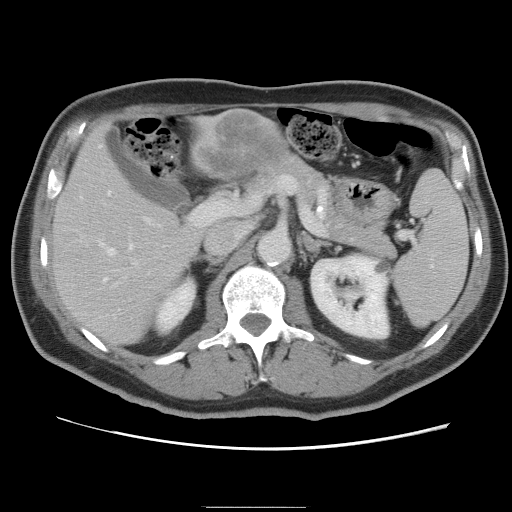
Contrast-enhanced abdominal CT, one axial slice. Soft-tissue window (W 400 / L 40 HU). 5 mm slice thickness. 512 × 512 image matrix, field of view 363 × 363 mm. Male patient, age 63 years. From the clinical record (not read from this slice): diagnosis: colorectal cancer liver metastases, imaged before liver resection; multiple liver metastases: no; largest metastasis: 9 cm; disease in both lobes: no.
Structures marked on this image (manually delineated by an expert):
- hepatic veins: box from (x=100, y=191) to (x=132, y=280) px
- liver: (x=51, y=109)–(x=291, y=345)
- planned liver remnant (the part of the liver to remain after resection): (x=50, y=147)–(x=200, y=345)
- portal vein (with intrahepatic branches): (x=112, y=205)–(x=204, y=287)
- liver metastasis: (x=197, y=114)–(x=282, y=181)